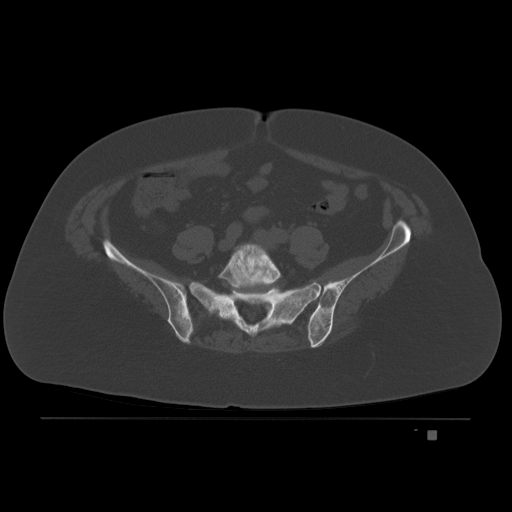
CT including the spine, one axial slice; slice 27 of 221 in the series (ordered by position); bone window (W 1800 / L 400 HU); 3 mm slice thickness; 512 × 512 image matrix. Patient: female, 63 years. From the clinical record (not read from this slice): primary cancer: breast.
Structures marked on this image (semi-automatically segmented with operator editing):
- L5 vertebra: bounding box (x1, y1, x2, y2) in pixels: (217, 243, 283, 289)